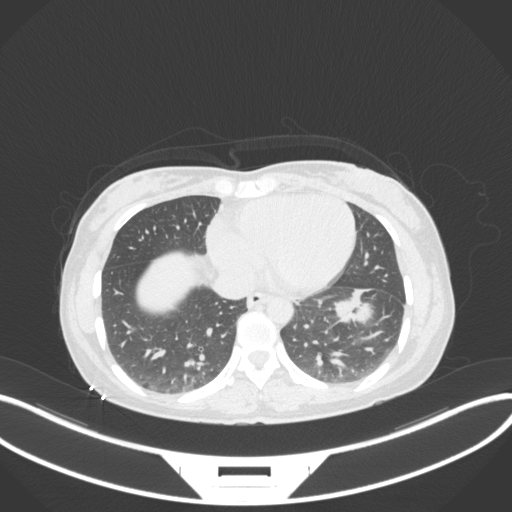
Chest CT, one axial slice. Position 120 of 361 along the scan axis. Reconstruction kernel B31f. 120 kVp. Lung window (W 1500 / L -600 HU). 512 × 512 image matrix, field of view 400 × 400 mm. Patient: female, 41 years. Case-level facts recorded for this patient, not image findings: clinical TNM (as recorded): T2a N3 M1b.
Annotated regions visible in this slice (bounding box drawn by a radiologist):
- lung tumour (recorded histology: adenocarcinoma): box from (x=335, y=286) to (x=381, y=325) px